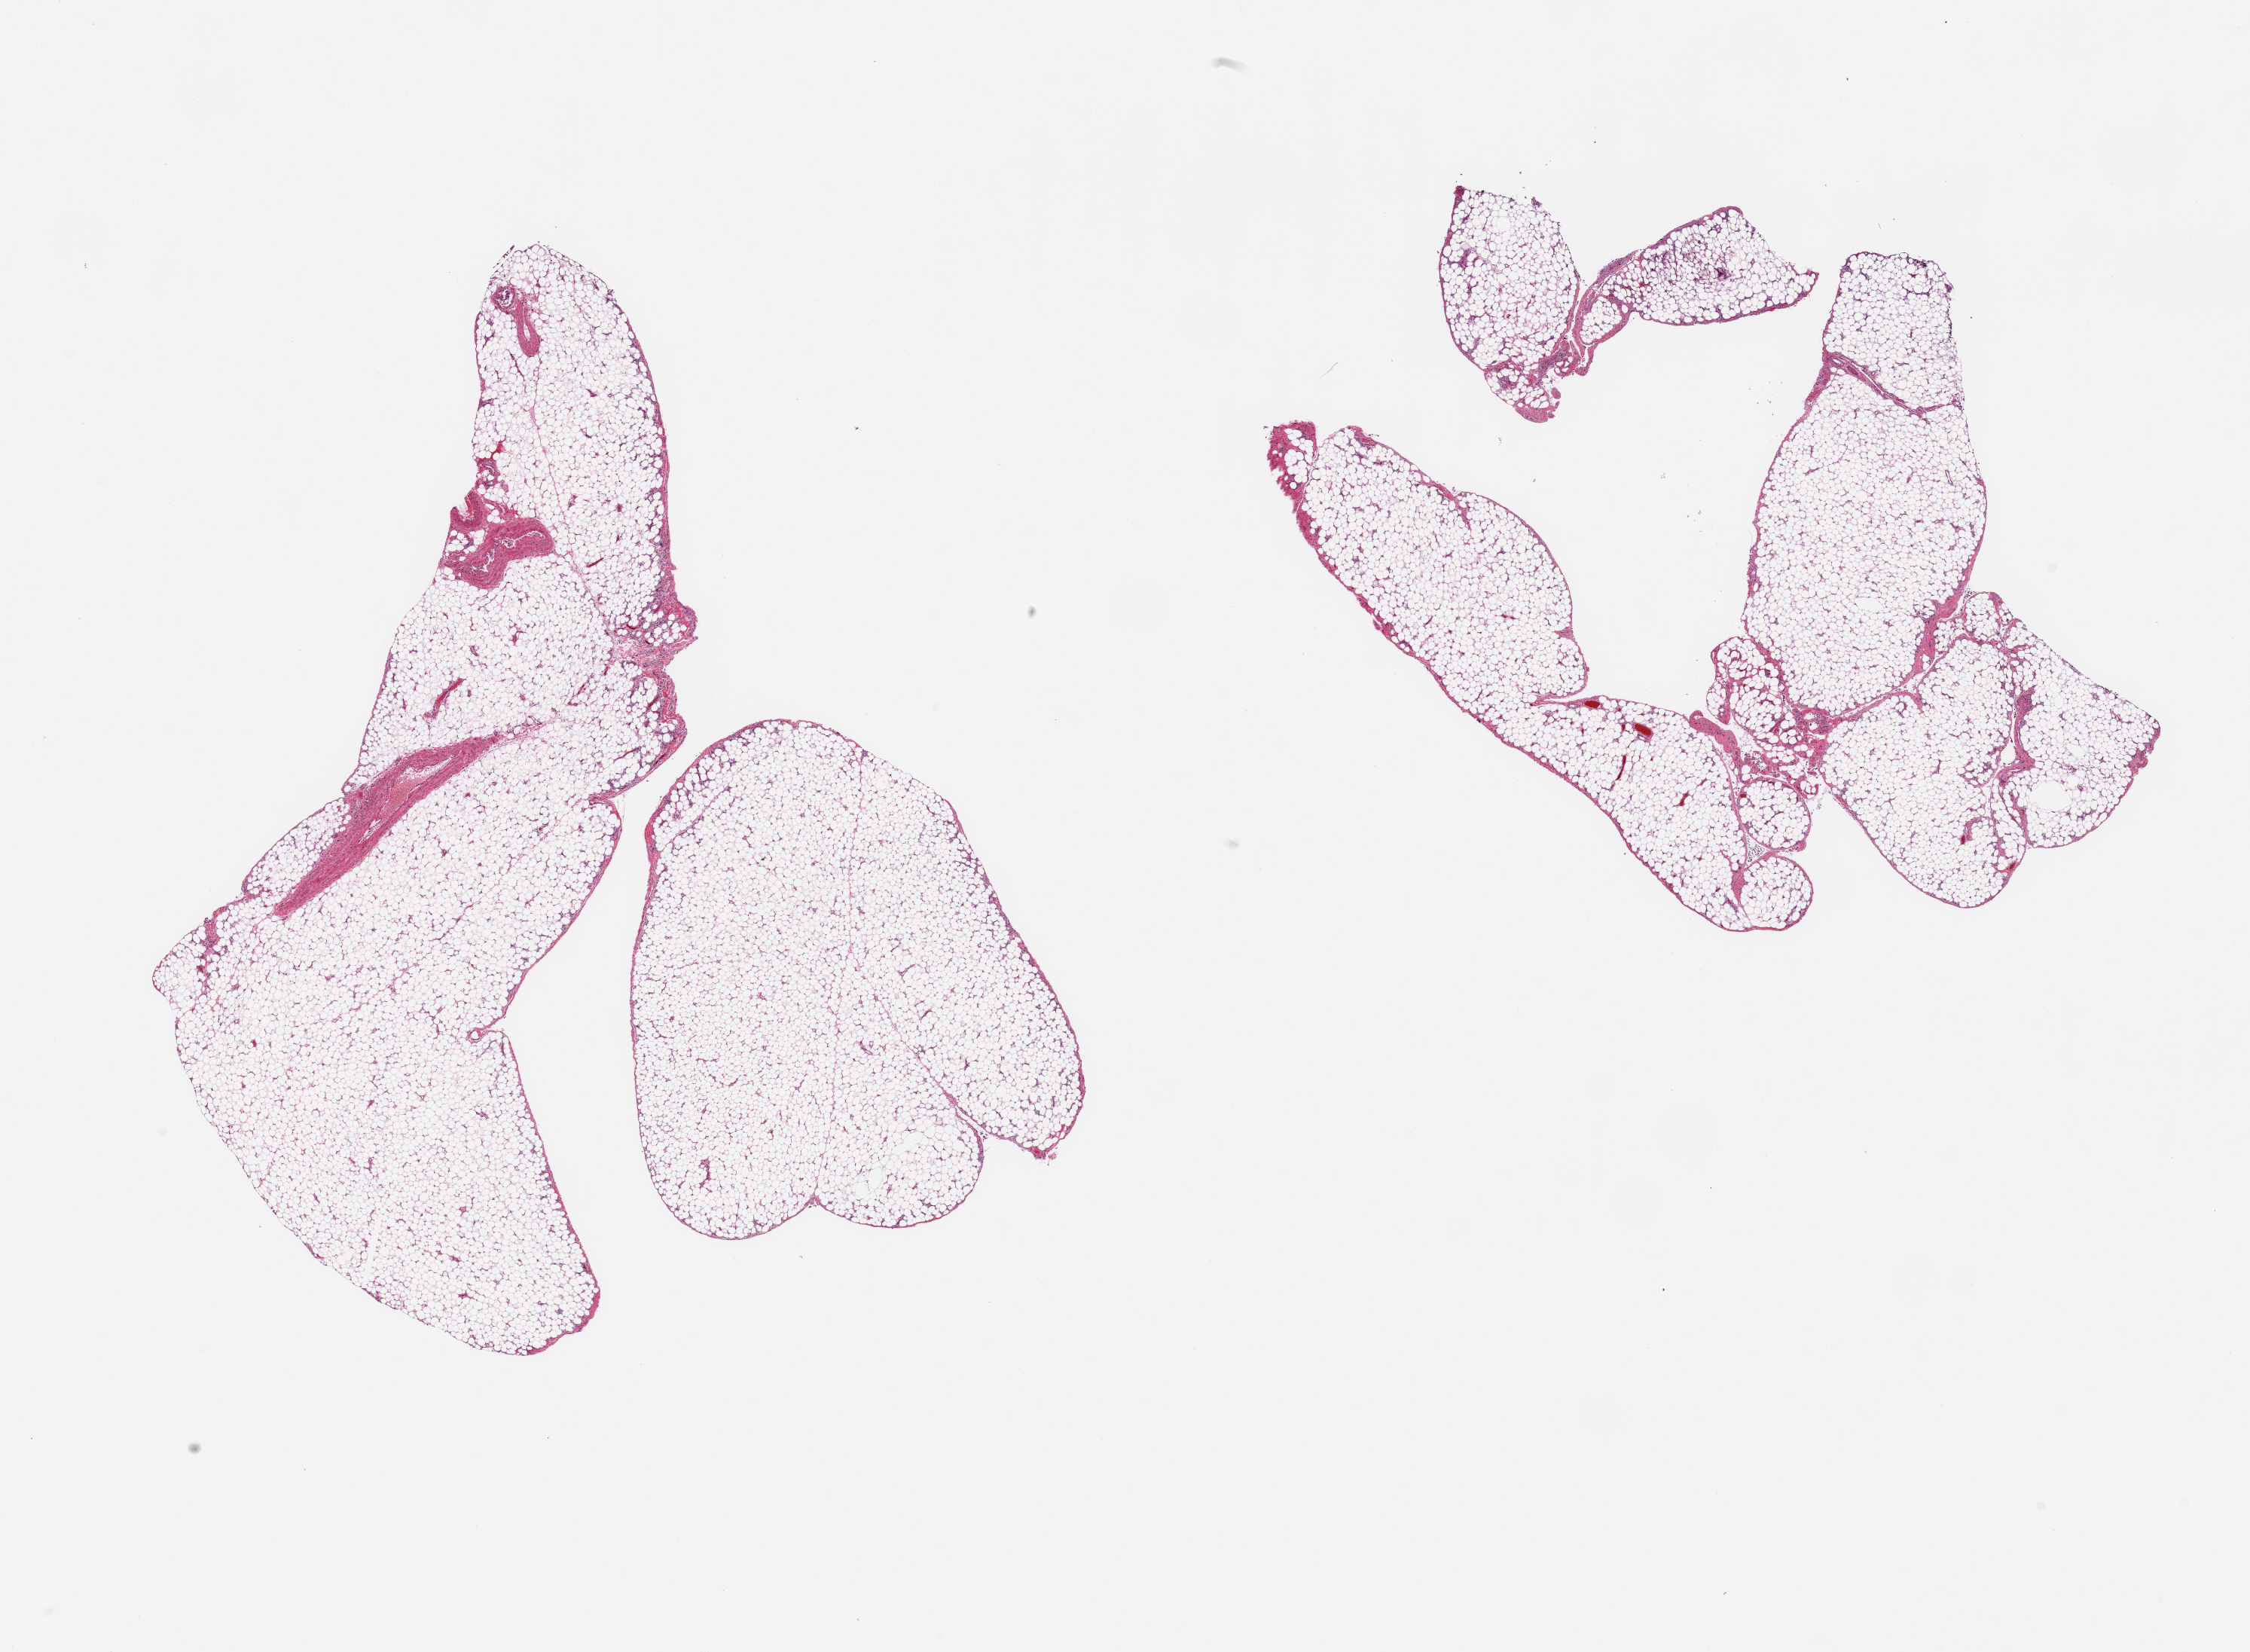
H&E whole-slide image, shown as a low-resolution overview of the whole scanned area (about 23.6 x 17.3 mm, from a 20x scan), PAXgene-fixed paraffin-embedded (PFPE) section, target tissue: omentum, donor tissue sample. Male donor.
Pathologist's review note for this sample: 2 pieces, ~10-15% fascia/vascular elements.